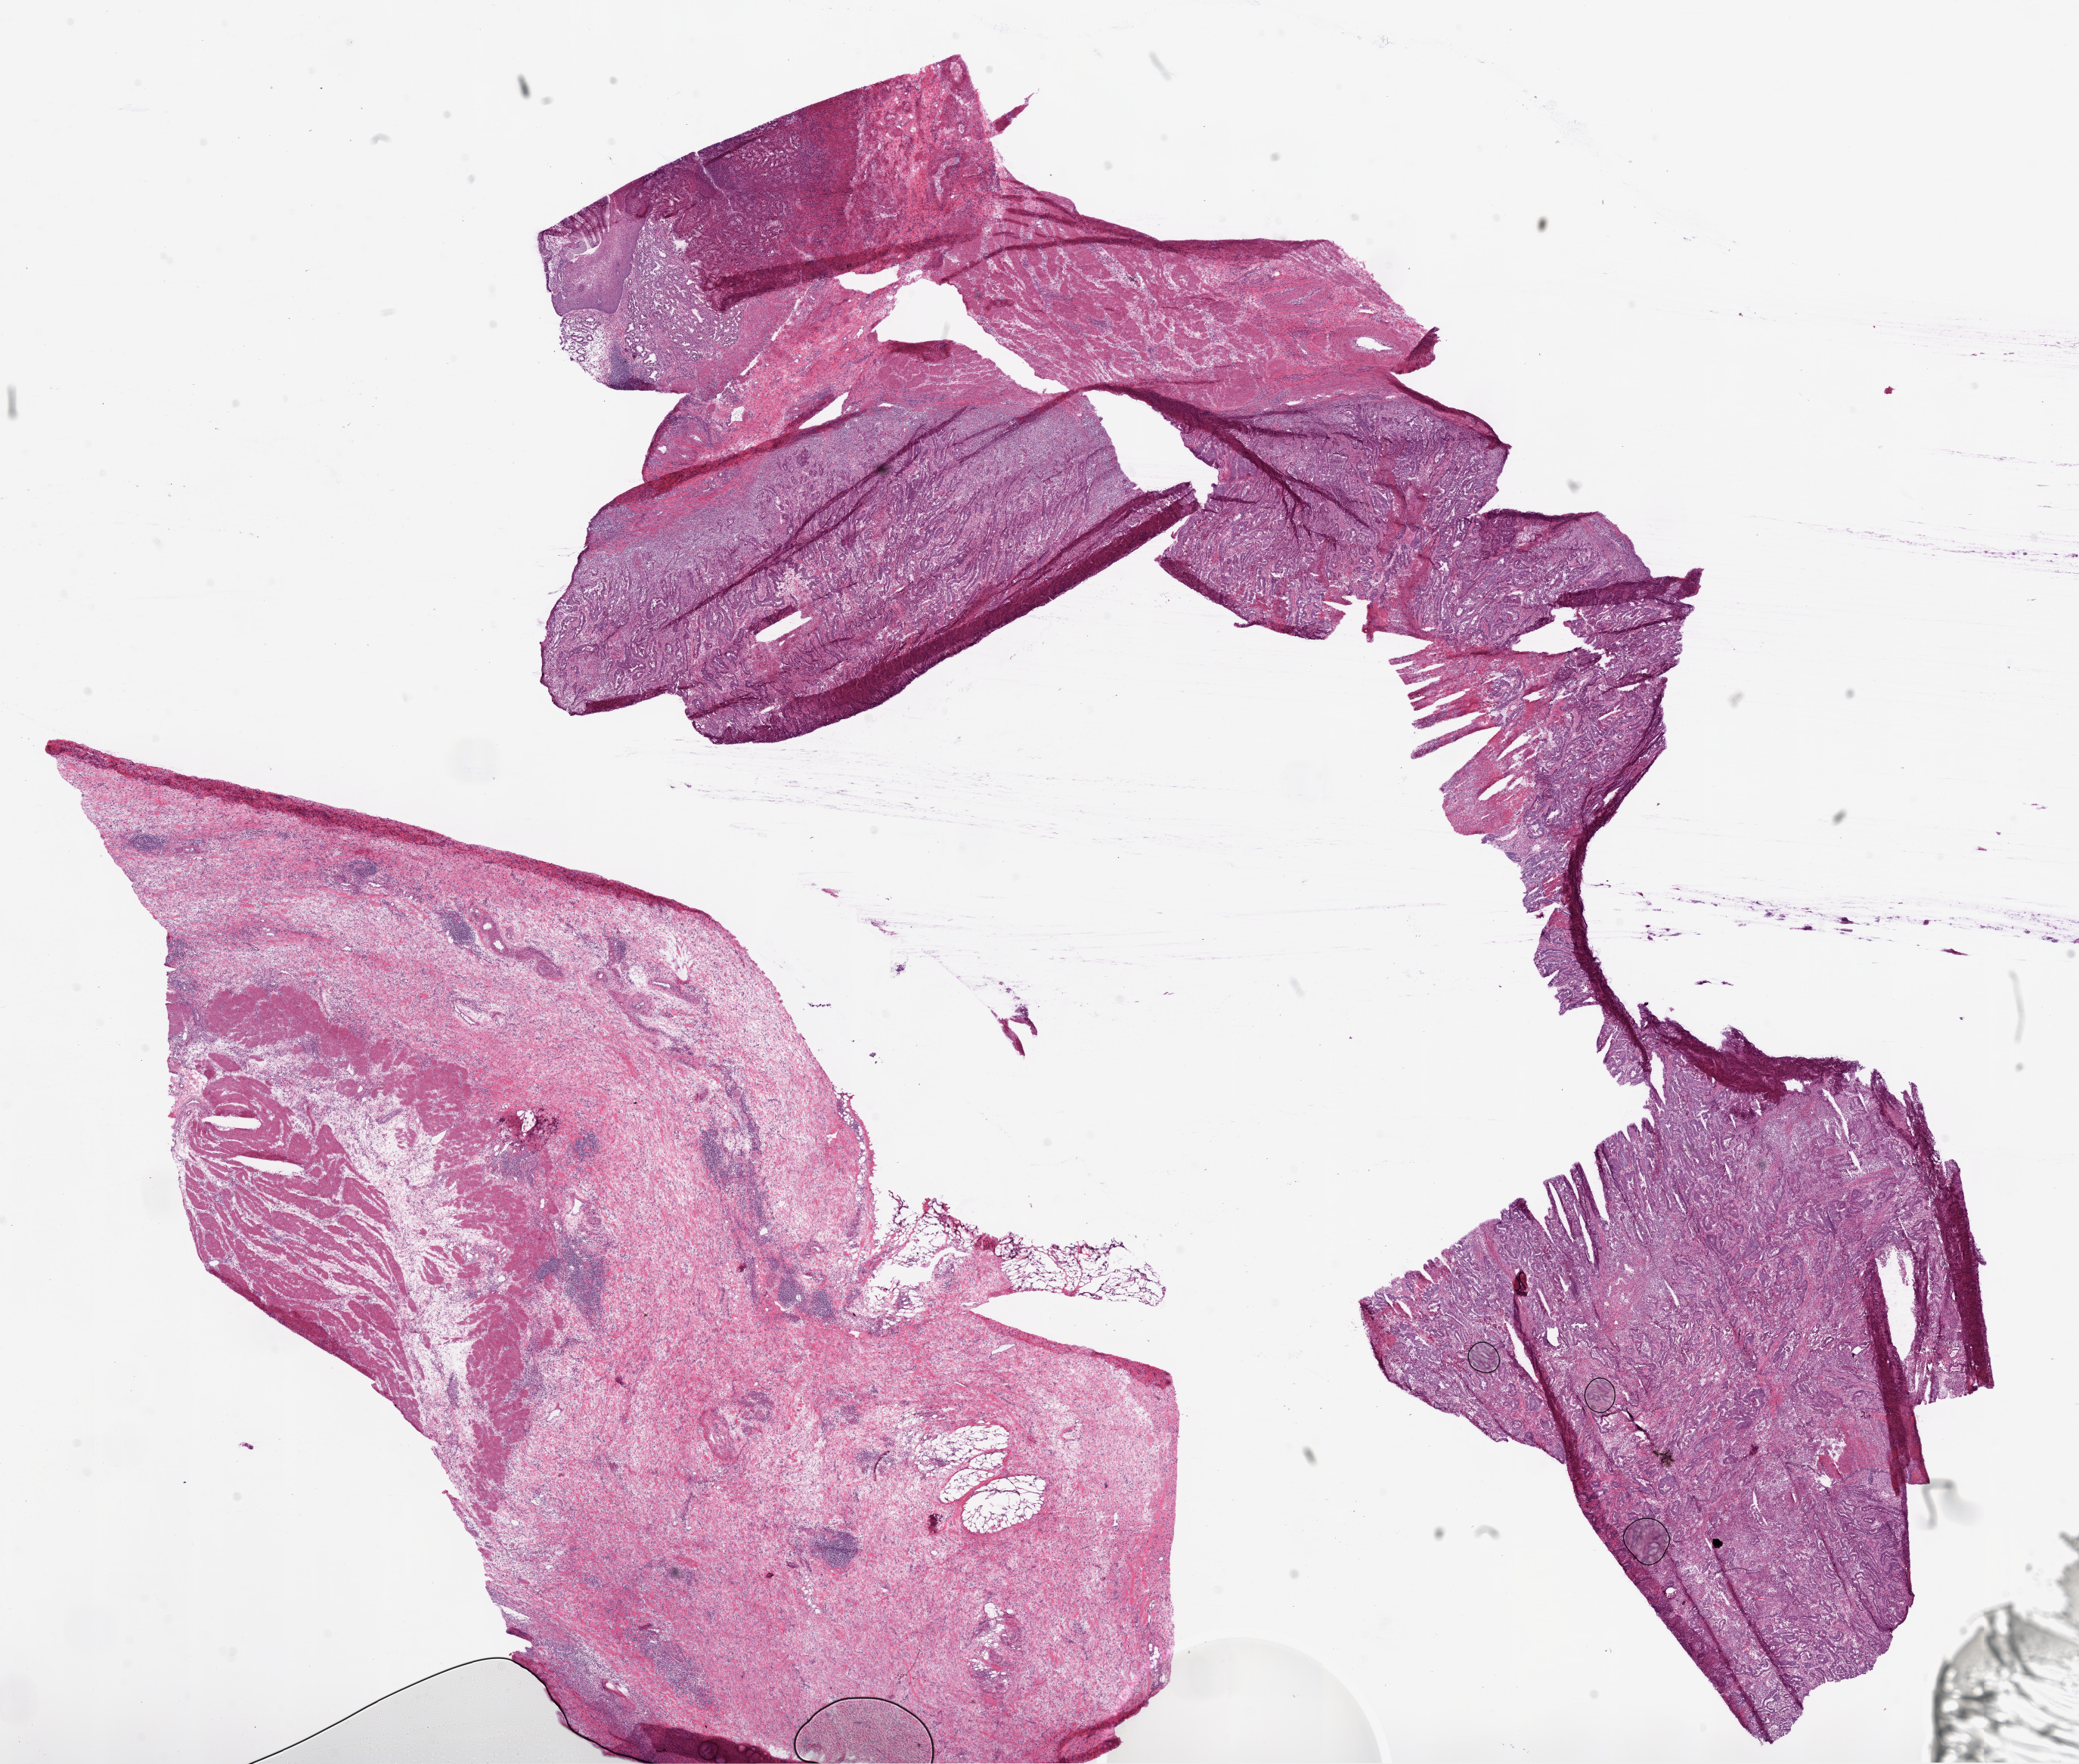
Whole-slide histology image, H&E-stained, a low-resolution overview of the entire scanned area, about 22.1 x 18.7 mm (slide scanned at 20x). Frozen section from the bottom of the tissue portion. Primary tumour sample from the stomach. Female patient; age at initial diagnosis 66 years. Histologic grade: G1 (well differentiated). Composition of this section per pathologist review: tumour cells 50%, tumour nuclei 70%, normal cells 40%, stromal cells 5%, necrosis 5%.
Histologic diagnosis: Adenocarcinoma, NOS (cardia, NOS).